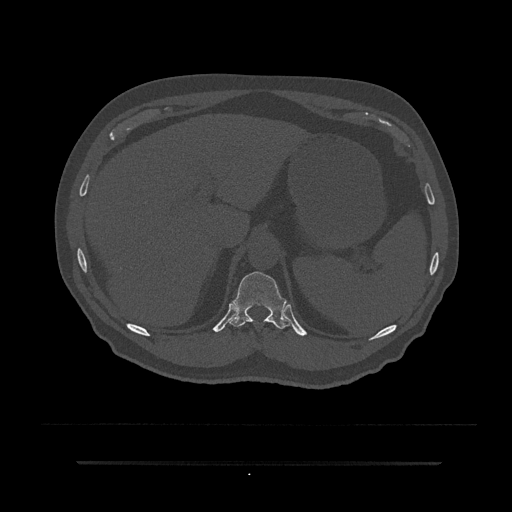
CT including the spine, one axial slice. Position 279 of 797 along the scan axis. Reconstruction kernel Br40s/3. 120 kVp. Bone window (W 1800 / L 400 HU). 0.5 mm slice thickness. 512 × 512 image matrix, field of view 464 × 464 mm. Male patient, age 59 years. From the clinical record (not read from this slice): primary cancer: bile ducts; vertebrae with lytic lesions (as recorded): T10.
Annotated regions visible in this slice (semi-automatic segmentation, software-assisted and operator-edited):
- T11 vertebra: bounding box [x1, y1, x2, y2] px = [230, 271, 292, 329]